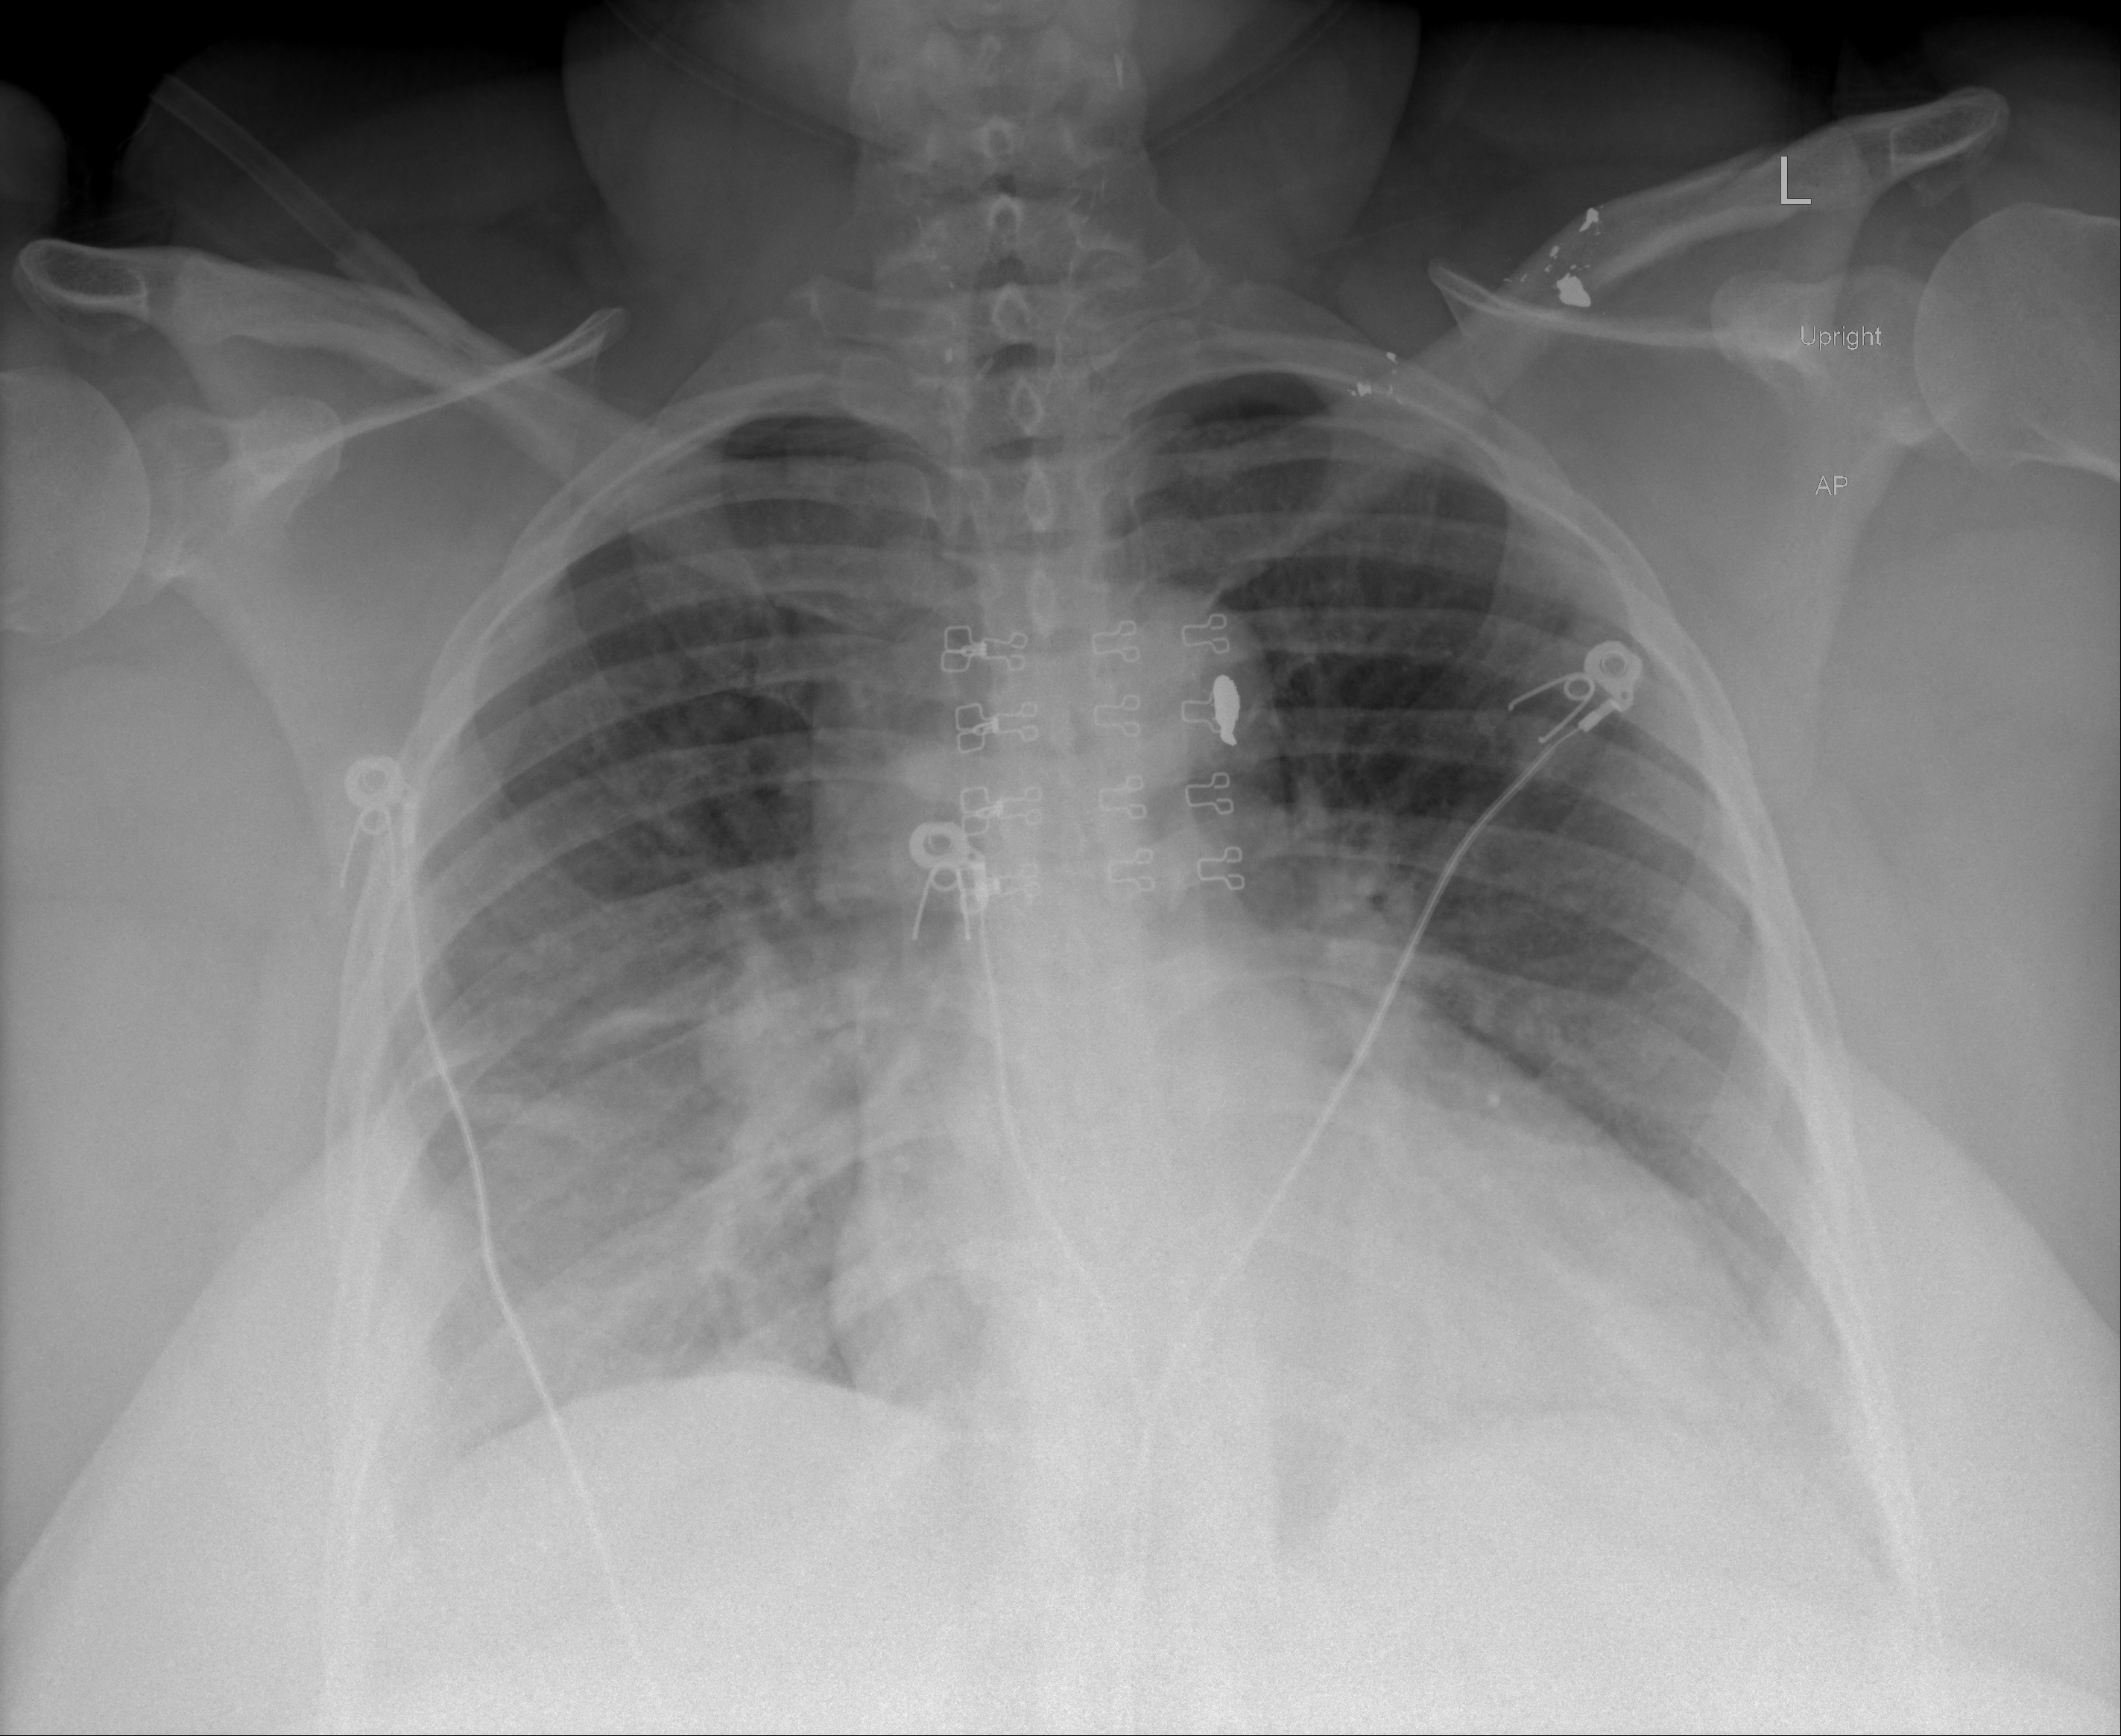
Portable chest radiograph, AP projection. Female patient, age 42 years; imaged 1 day after the COVID-19 diagnosis.
Radiologist key findings (as recorded): Bibasilar linear opacities may be related to atelectasis or infection.